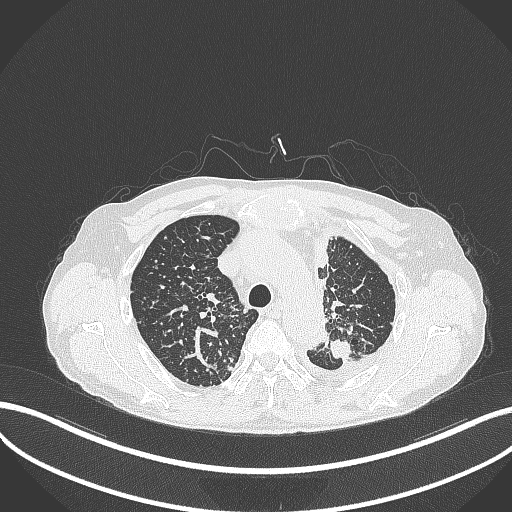
Chest CT, one axial slice. Reconstruction kernel B70f. 120 kVp. Lung window (W 1500 / L -600 HU). 1 mm slice thickness. 512 × 512 image matrix. Male patient, age 58 years. Case-level facts recorded for this patient, not image findings: clinical TNM (as recorded): T1c N3 M1.
Structures marked on this image (rectangle marked by the reading radiologist):
- lung tumour (recorded histology: adenocarcinoma): bounding box (x1, y1, x2, y2) in pixels: (326, 334, 358, 362)